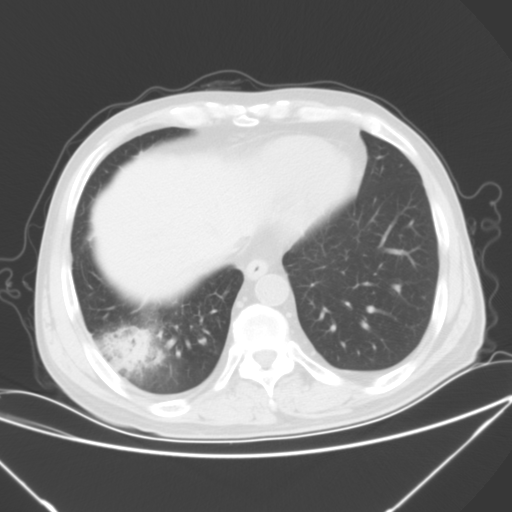
Chest CT, one axial slice; position 18 of 57 along the scan axis; 120 kVp; lung window (W 1500 / L -600 HU); 5 mm slice thickness; 512 × 512 image matrix, field of view 364 × 364 mm. Patient: male, 54 years. From the clinical record (not read from this slice): clinical TNM (as recorded): T2 N1 M0; histopathological grade: G3.
Annotated regions visible in this slice (rectangle marked by the reading radiologist):
- lung tumour (recorded histology: adenocarcinoma): box from (x=107, y=327) to (x=149, y=371) px